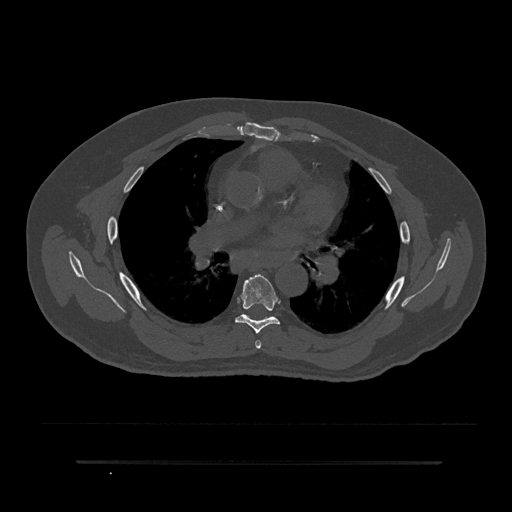
CT including the spine, one axial slice. Position 528 of 797 along the scan axis. Reconstruction kernel Br40s/3. Bone window (W 1800 / L 400 HU). 0.5 mm slice thickness. 512 × 512 image matrix, field of view 464 × 464 mm. Male patient, age 59 years. Case-level facts recorded for this patient, not image findings: primary cancer: bile ducts; vertebrae with lytic lesions (as recorded): T10.
Annotated regions visible in this slice (semi-automatically segmented with operator editing):
- T5 vertebra: bounding box <255,340,261,349> (left, top, right, bottom; pixels)
- T6 vertebra: <235,274,280,334>